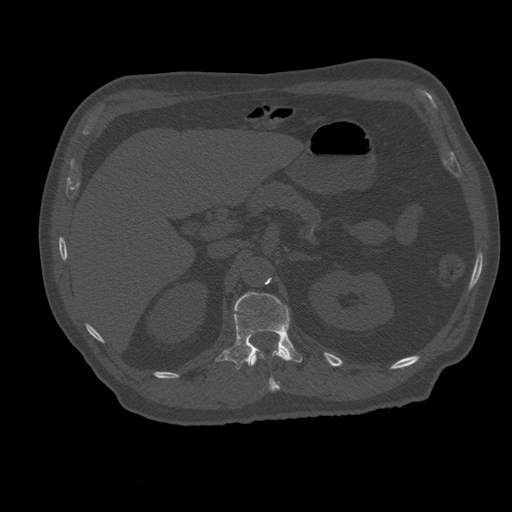
CT including the spine, one axial slice. Slice 244 of 399 in the series (ordered by position). Reconstruction kernel STANDARD. 120 kVp. Bone window (W 1800 / L 400 HU). 512 × 512 image matrix. Patient age 73 years. Case-level facts recorded for this patient, not image findings: primary cancer: prostate.
Structures marked on this image (semi-automatically segmented with operator editing):
- L1 vertebra: box from (x=215, y=292) to (x=303, y=370) px
- T12 vertebra: (x=249, y=346)–(x=291, y=392)